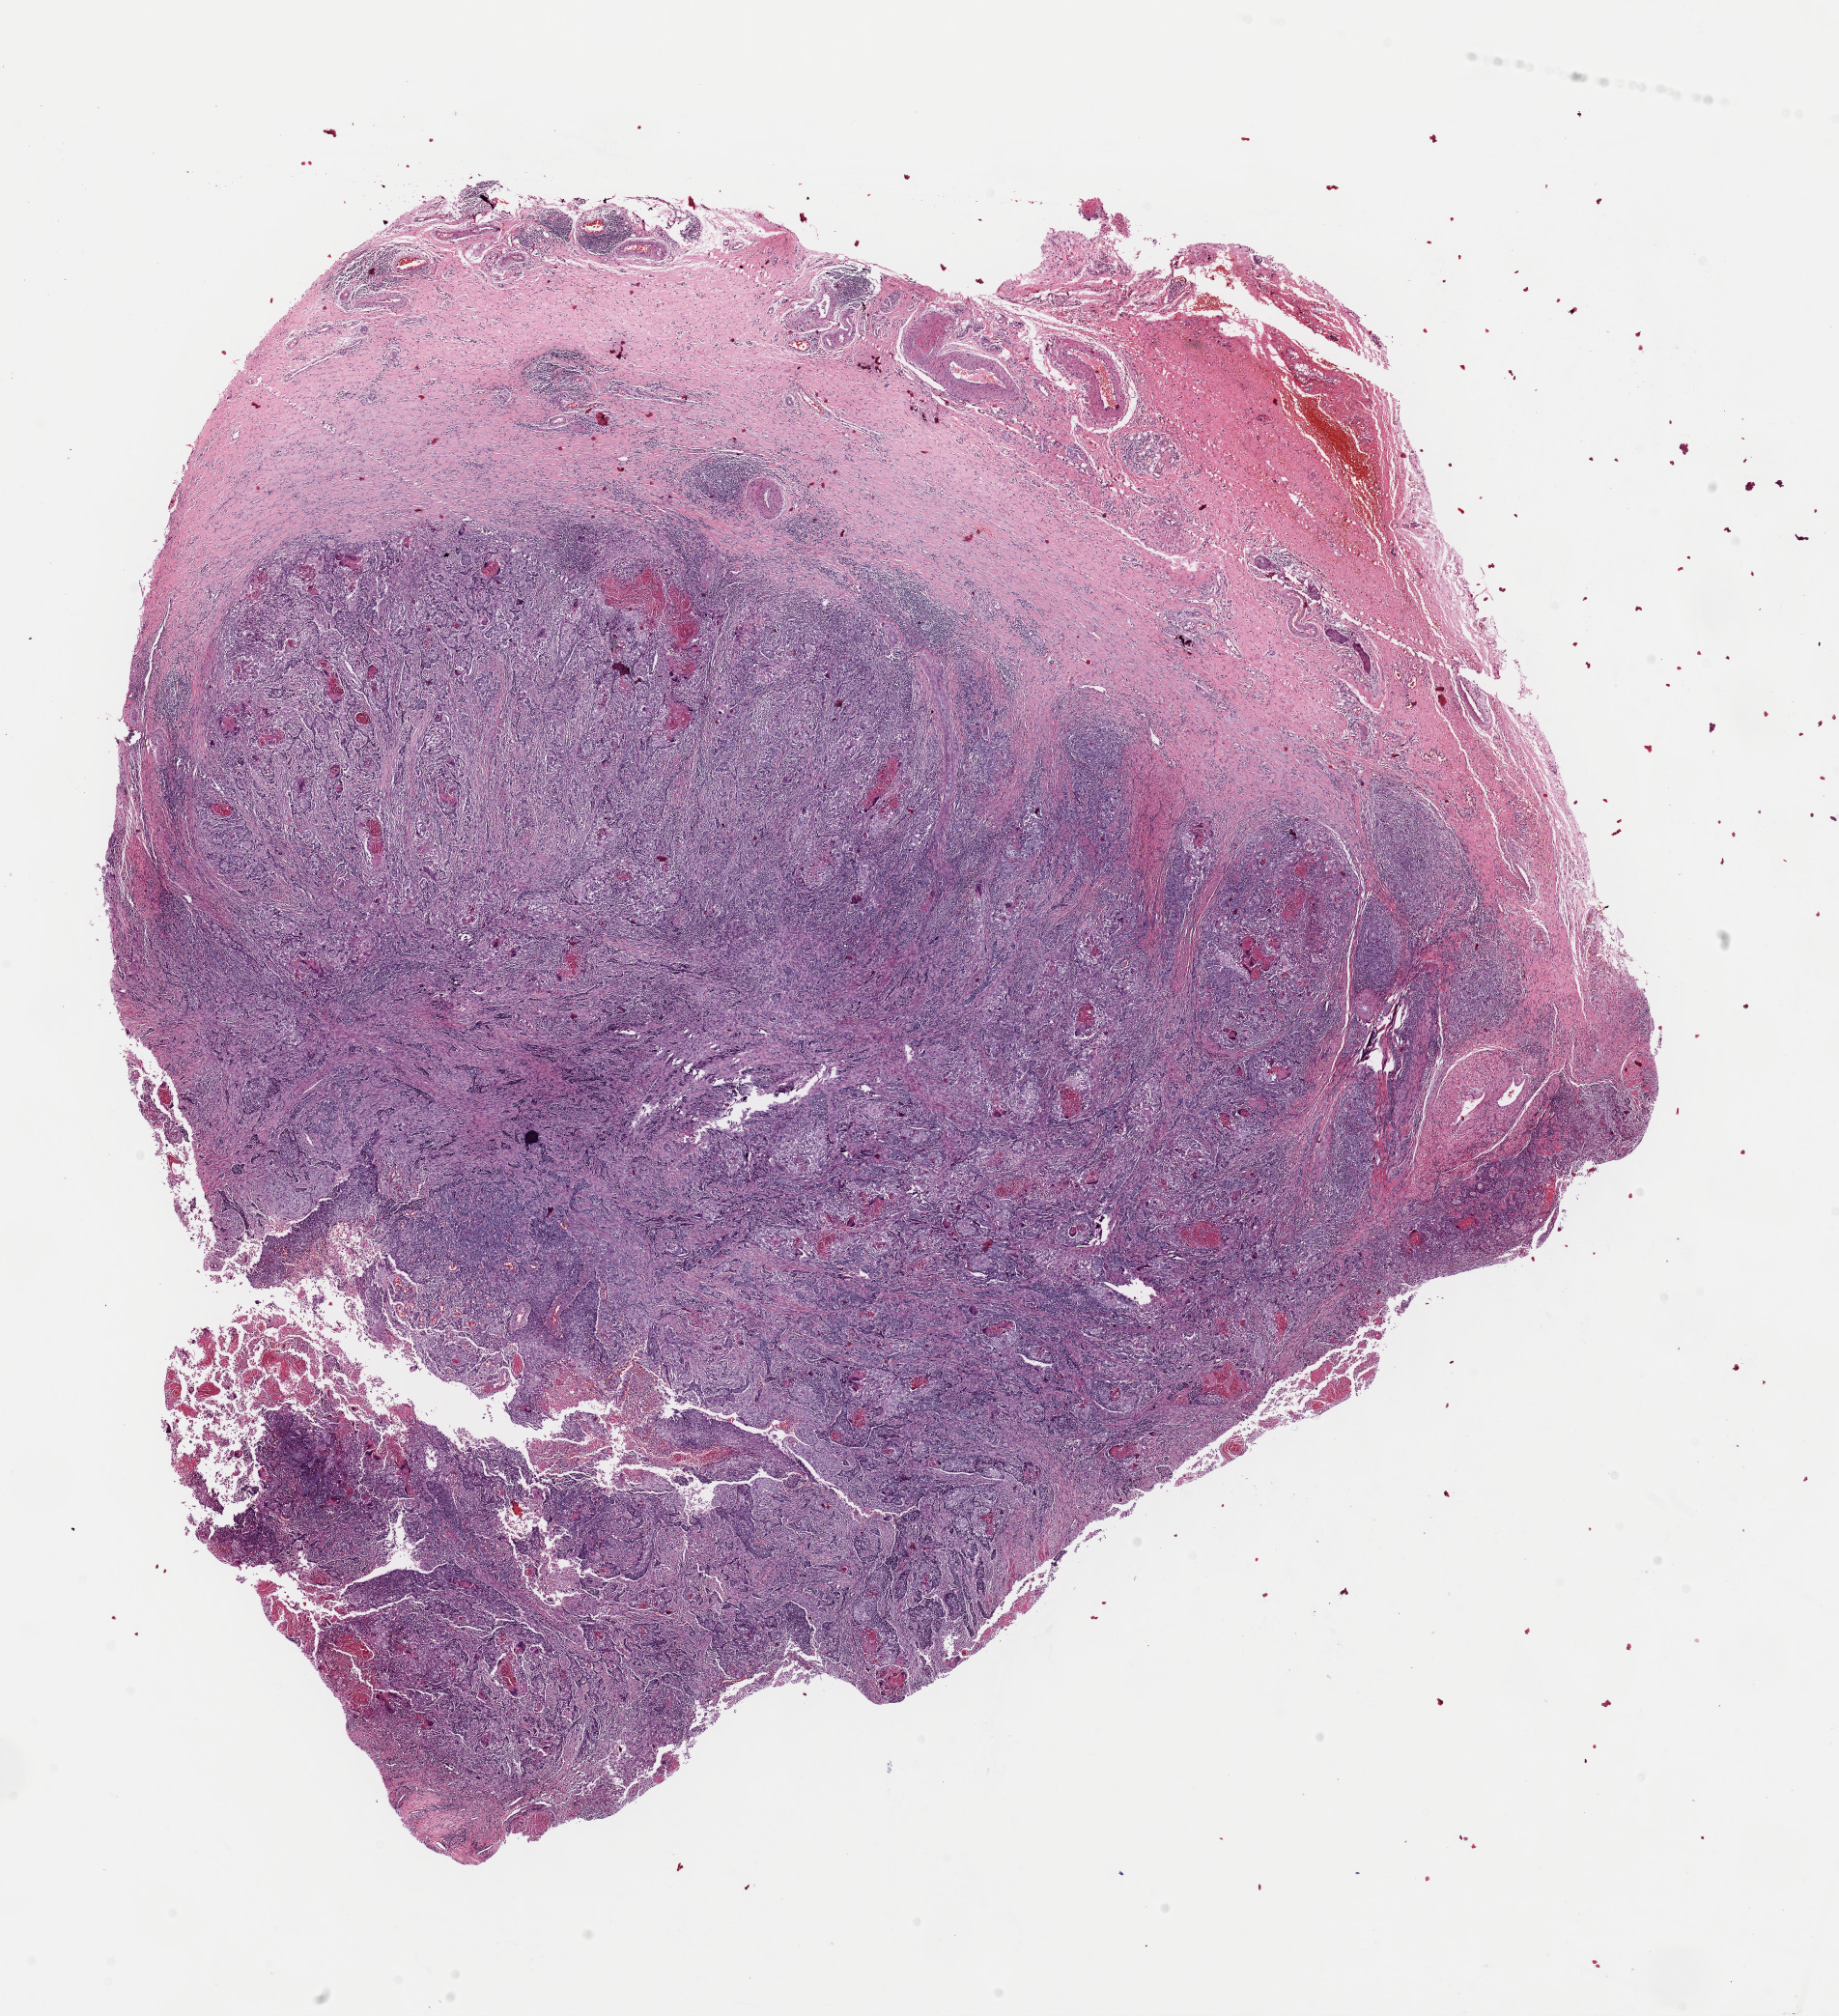
Whole-slide histology image, H&E, shown as a low-resolution overview of the whole scanned area (about 15.0 x 16.5 mm). FFPE section. Sample: primary tumour, esophagus. Patient: male, age at initial diagnosis 73 years. Histologic grade: G3 (poorly differentiated).
Histologic diagnosis: Squamous cell carcinoma, NOS (middle third of esophagus). AJCC pathologic stage: III (6th edition). TNM: T3 N1 M0.